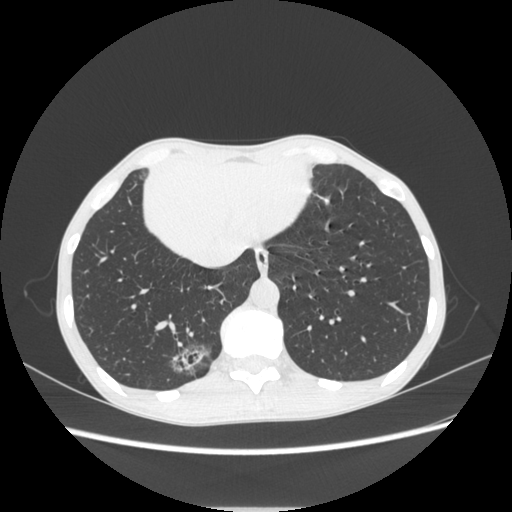
Chest CT, one axial slice. Reconstruction kernel STANDARD. 120 kVp. Lung window (W 1500 / L -600 HU). 512 × 512 image matrix, field of view 350 × 350 mm. Female patient, age 51 years. Case-level facts recorded for this patient, not image findings: clinical TNM (as recorded): T1c N0 M0.
Annotated regions visible in this slice (bounding box drawn by a radiologist):
- lung tumour (recorded histology: adenocarcinoma): bounding box [x1, y1, x2, y2] px = [163, 337, 216, 385]